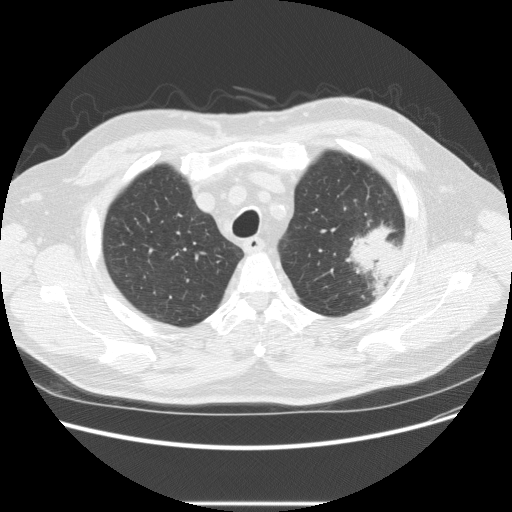
Low-dose screening chest CT, one axial slice. Position 186 of 233 along the scan axis. Reconstruction kernel STANDARD. 120 kVp. Lung window (W 1500 / L -600 HU). 2.5 mm slice thickness. 512 × 512 image matrix, field of view 380 × 380 mm.
Annotated regions visible in this slice (manually delineated by an expert):
- lesion 1 (tumor, upper lobe of left lung): bounding box [x1, y1, x2, y2] px = [346, 223, 401, 291]